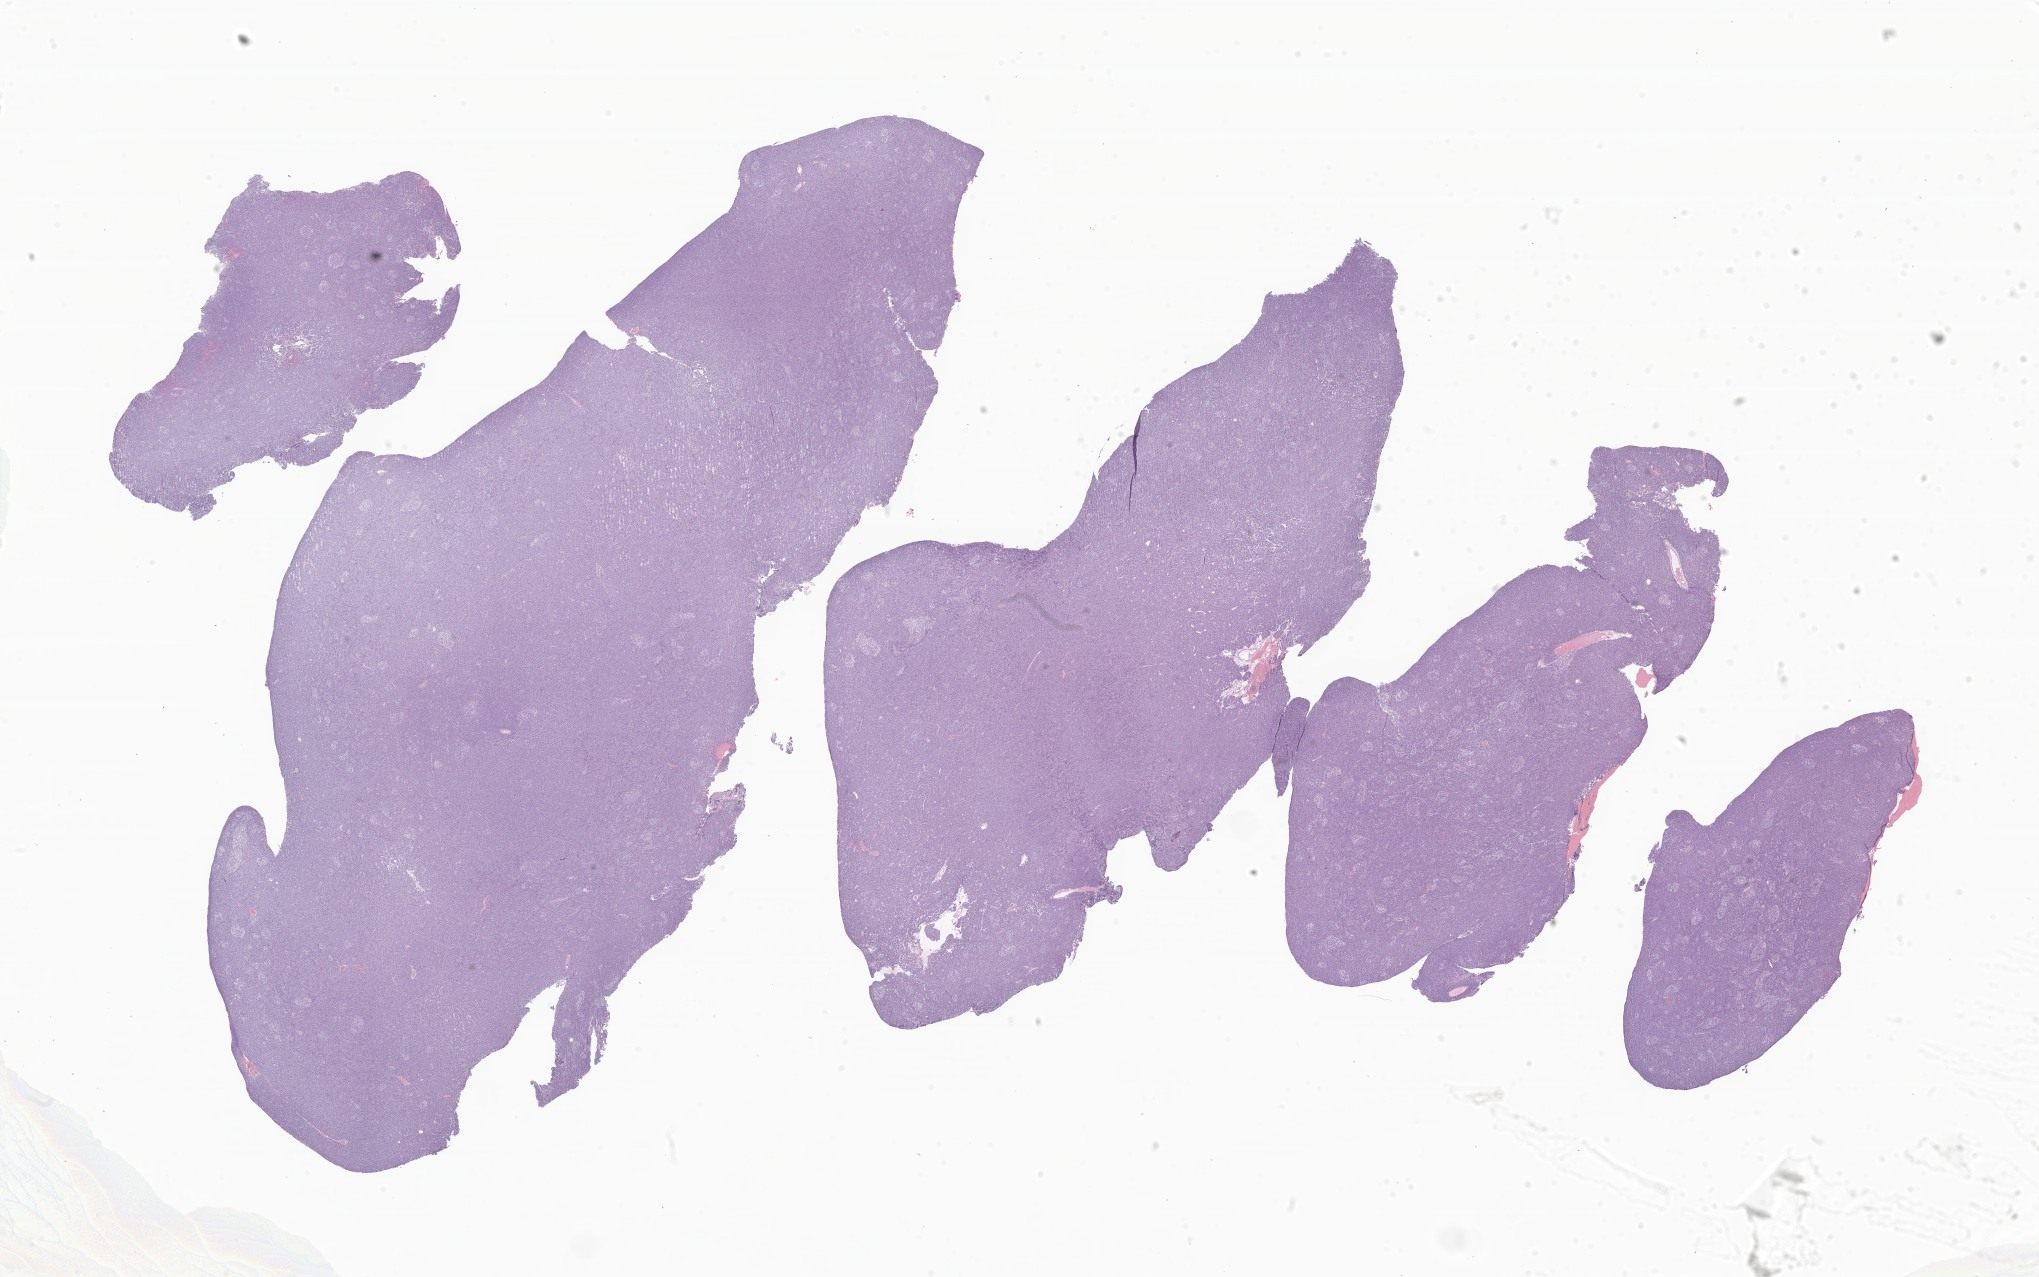
Digitized hematoxylin and eosin (H&E)-stained section of tumor tissue from the cerebellum, whole scanned area (about 34.4 x 21.5 mm) shown as a low-resolution overview; FFPE section. Patient: male, age 187 months (15 years 7 months).
- diagnosis (ICD-O-3 morphology term): Neoplasm, uncertain whether benign or malignant